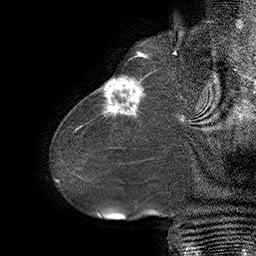
Breast MRI (dynamic contrast-enhanced), one sagittal slice; slice 11 of 55 in the series (ordered by position); dynamic contrast-enhanced series, time point 2 of 6 at this slice position (early post-contrast); 1.5 T; TE 4.5 ms, TR 32.4 ms; 3 mm slice thickness; 256 × 256 image matrix. Female patient. Case-level facts recorded for this patient, not image findings: setting: breast cancer imaged before/during neoadjuvant chemotherapy; receptor status: HER2-positive.
Annotated regions visible in this slice (semi-automatically segmented with operator editing):
- analysis volume of interest (the breast-tissue region the enhancement analysis was run in; not a lesion): bounding box [x1, y1, x2, y2] px = [80, 64, 163, 134]
- tumour enhancement mask (voxels above the 100 % enhancement threshold inside the analysis volume of interest): [102, 75, 148, 116]